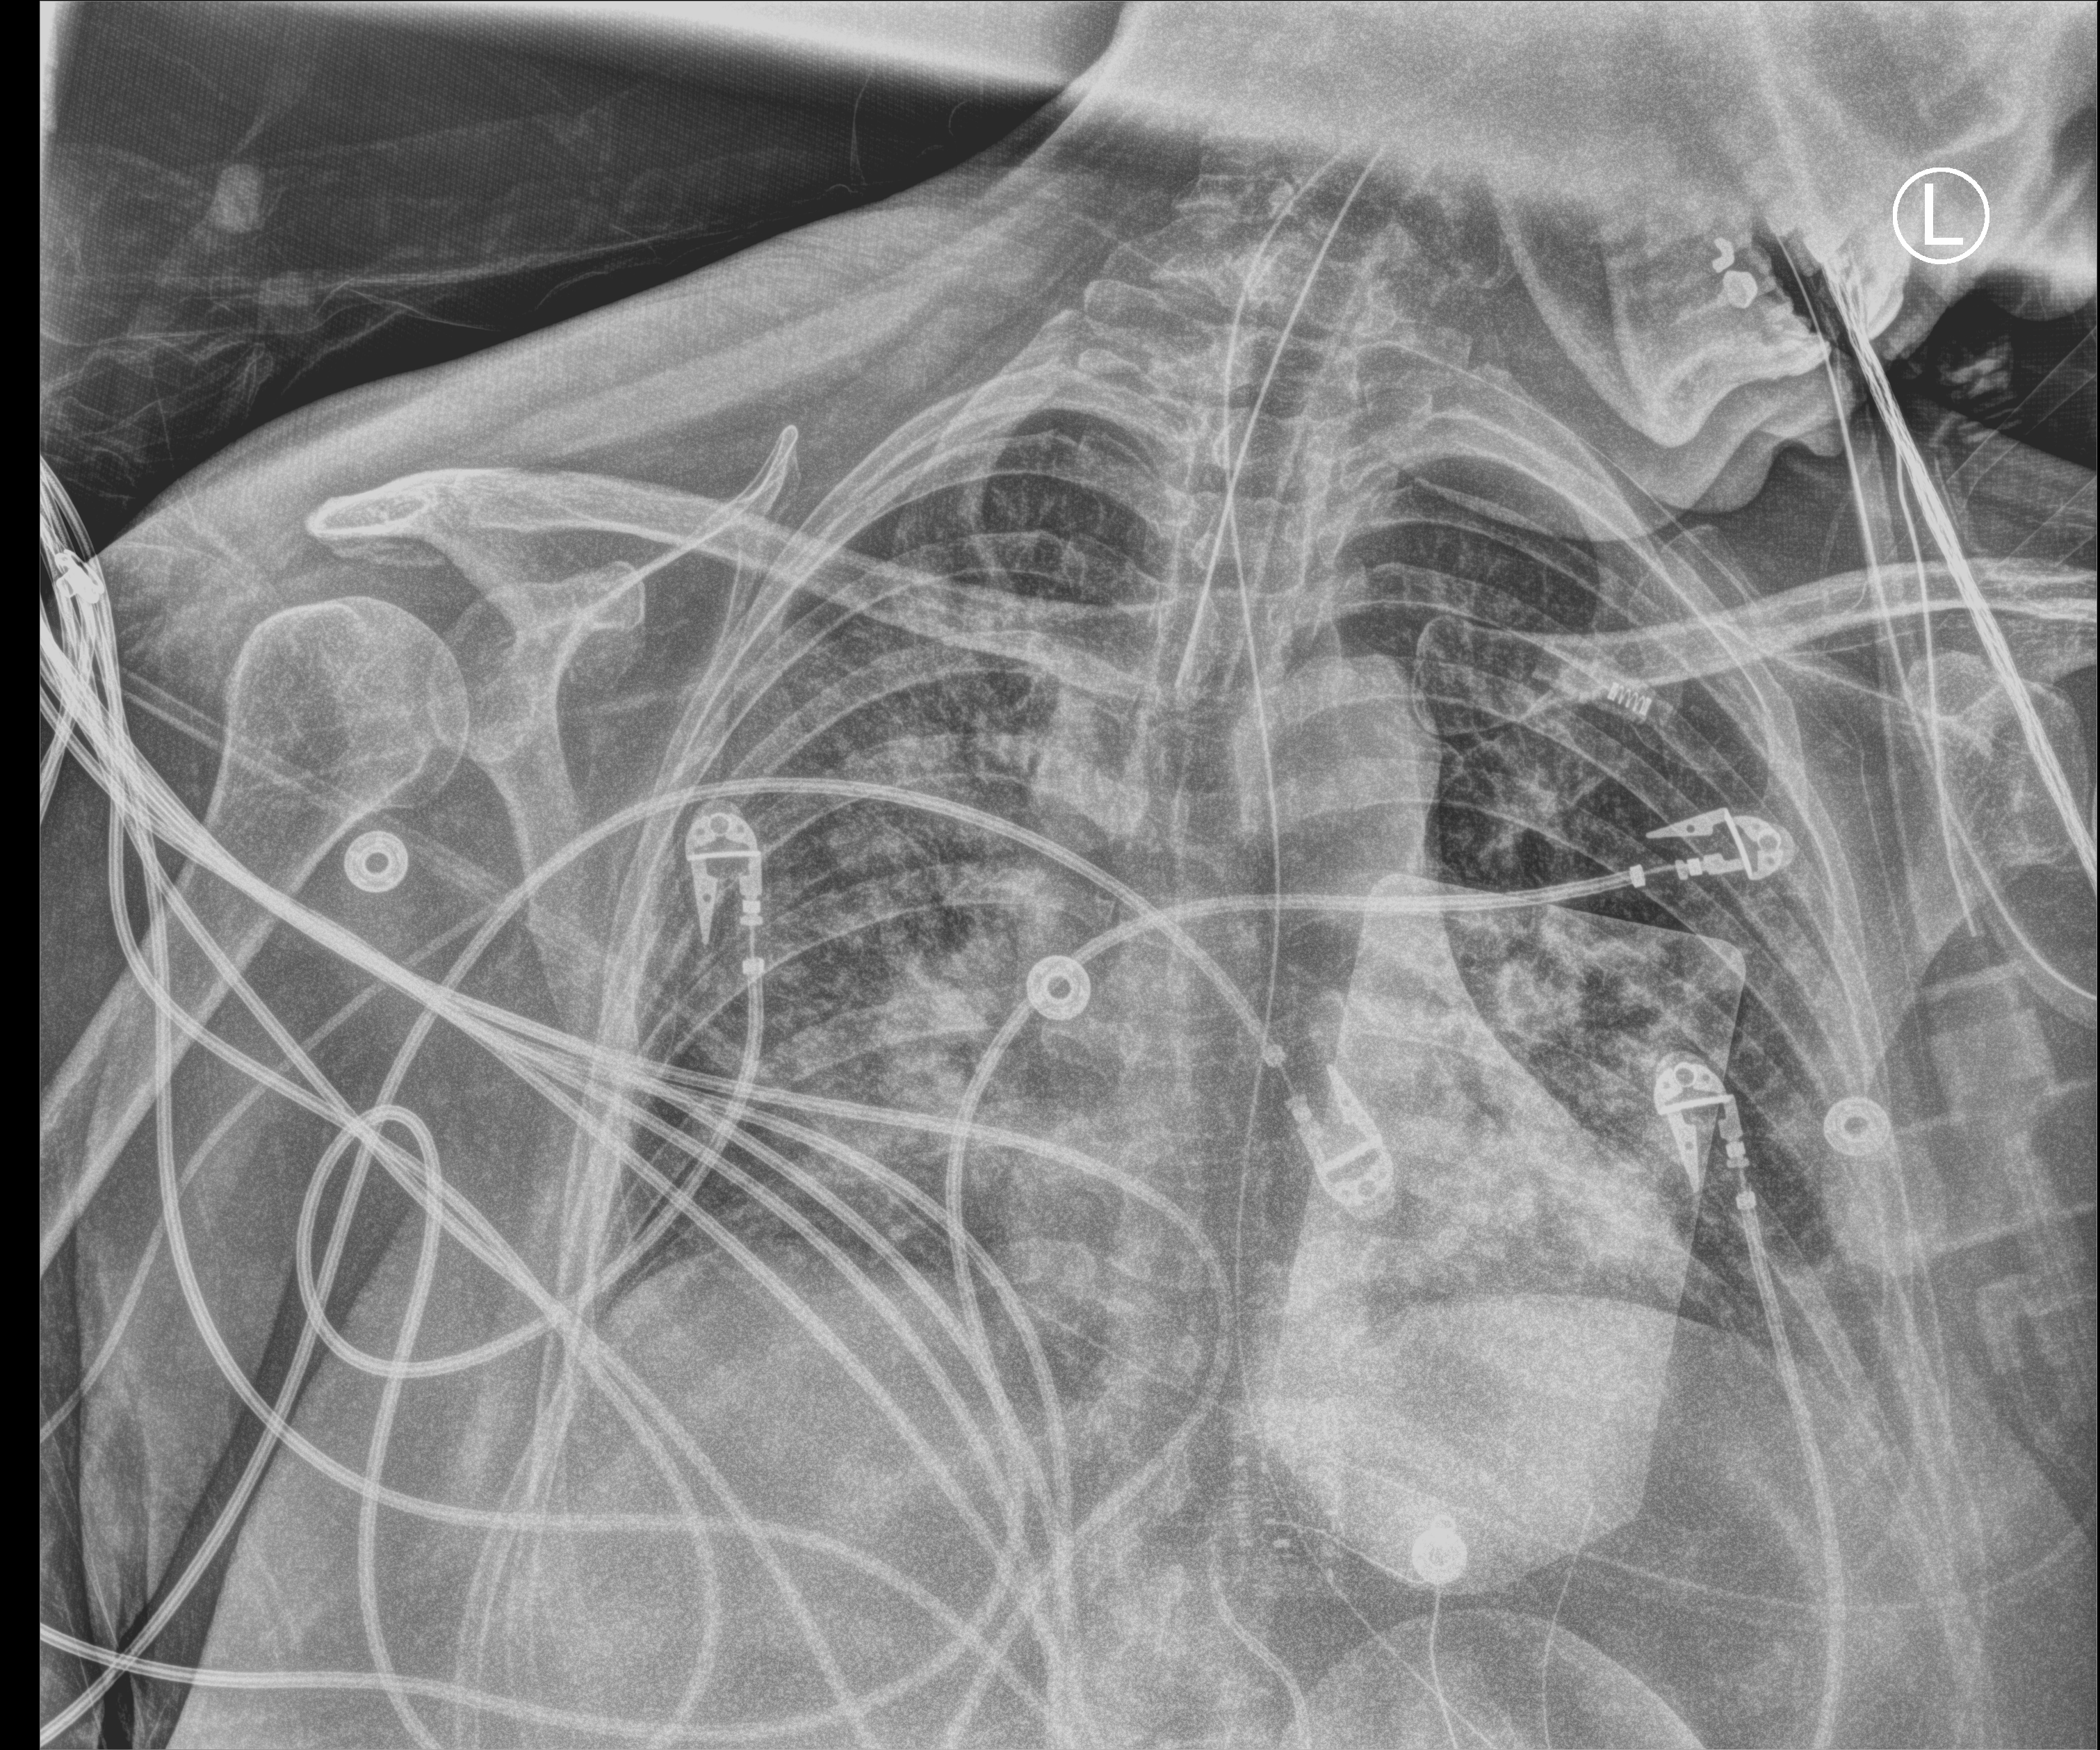
Portable chest radiograph; anteroposterior (AP) projection. Patient hospitalised with COVID-19; female, aged 18–59 years.
Hospital-stay facts (about this admission, not read from this image; timing relative to this image not recorded):
- admitted to intensive care during this hospital stay: yes